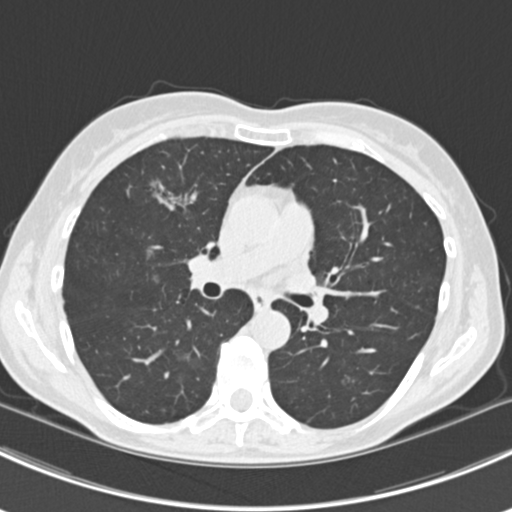
Low-dose screening chest CT, axial slice, baseline annual screen, lung window (W 1500 / L -600 HU), 2 mm slice thickness, 120 kVp. Female, age 63 years at enrolment. Current smoker at enrolment.
Expert-annotated lung lesion, box from (x=144, y=170) to (x=202, y=225) px. The screening reader recorded 10 non-calcified nodules or masses ≥4 mm on this exam (right lower lobe, right lower lobe, left lower lobe, left lower lobe, right middle lobe, right lower lobe, left lower lobe, left upper lobe, right upper lobe, left upper lobe); which of them this box marks is not recorded. Lung cancer was diagnosed 751 days after this screen (after the third annual screen): bronchiolo-alveolar adenocarcinoma, NOS, right upper lobe, right middle lobe, right lower lobe, left upper lobe, left lower lobe, moderately differentiated (G2), stage IV (AJCC 6th edition).